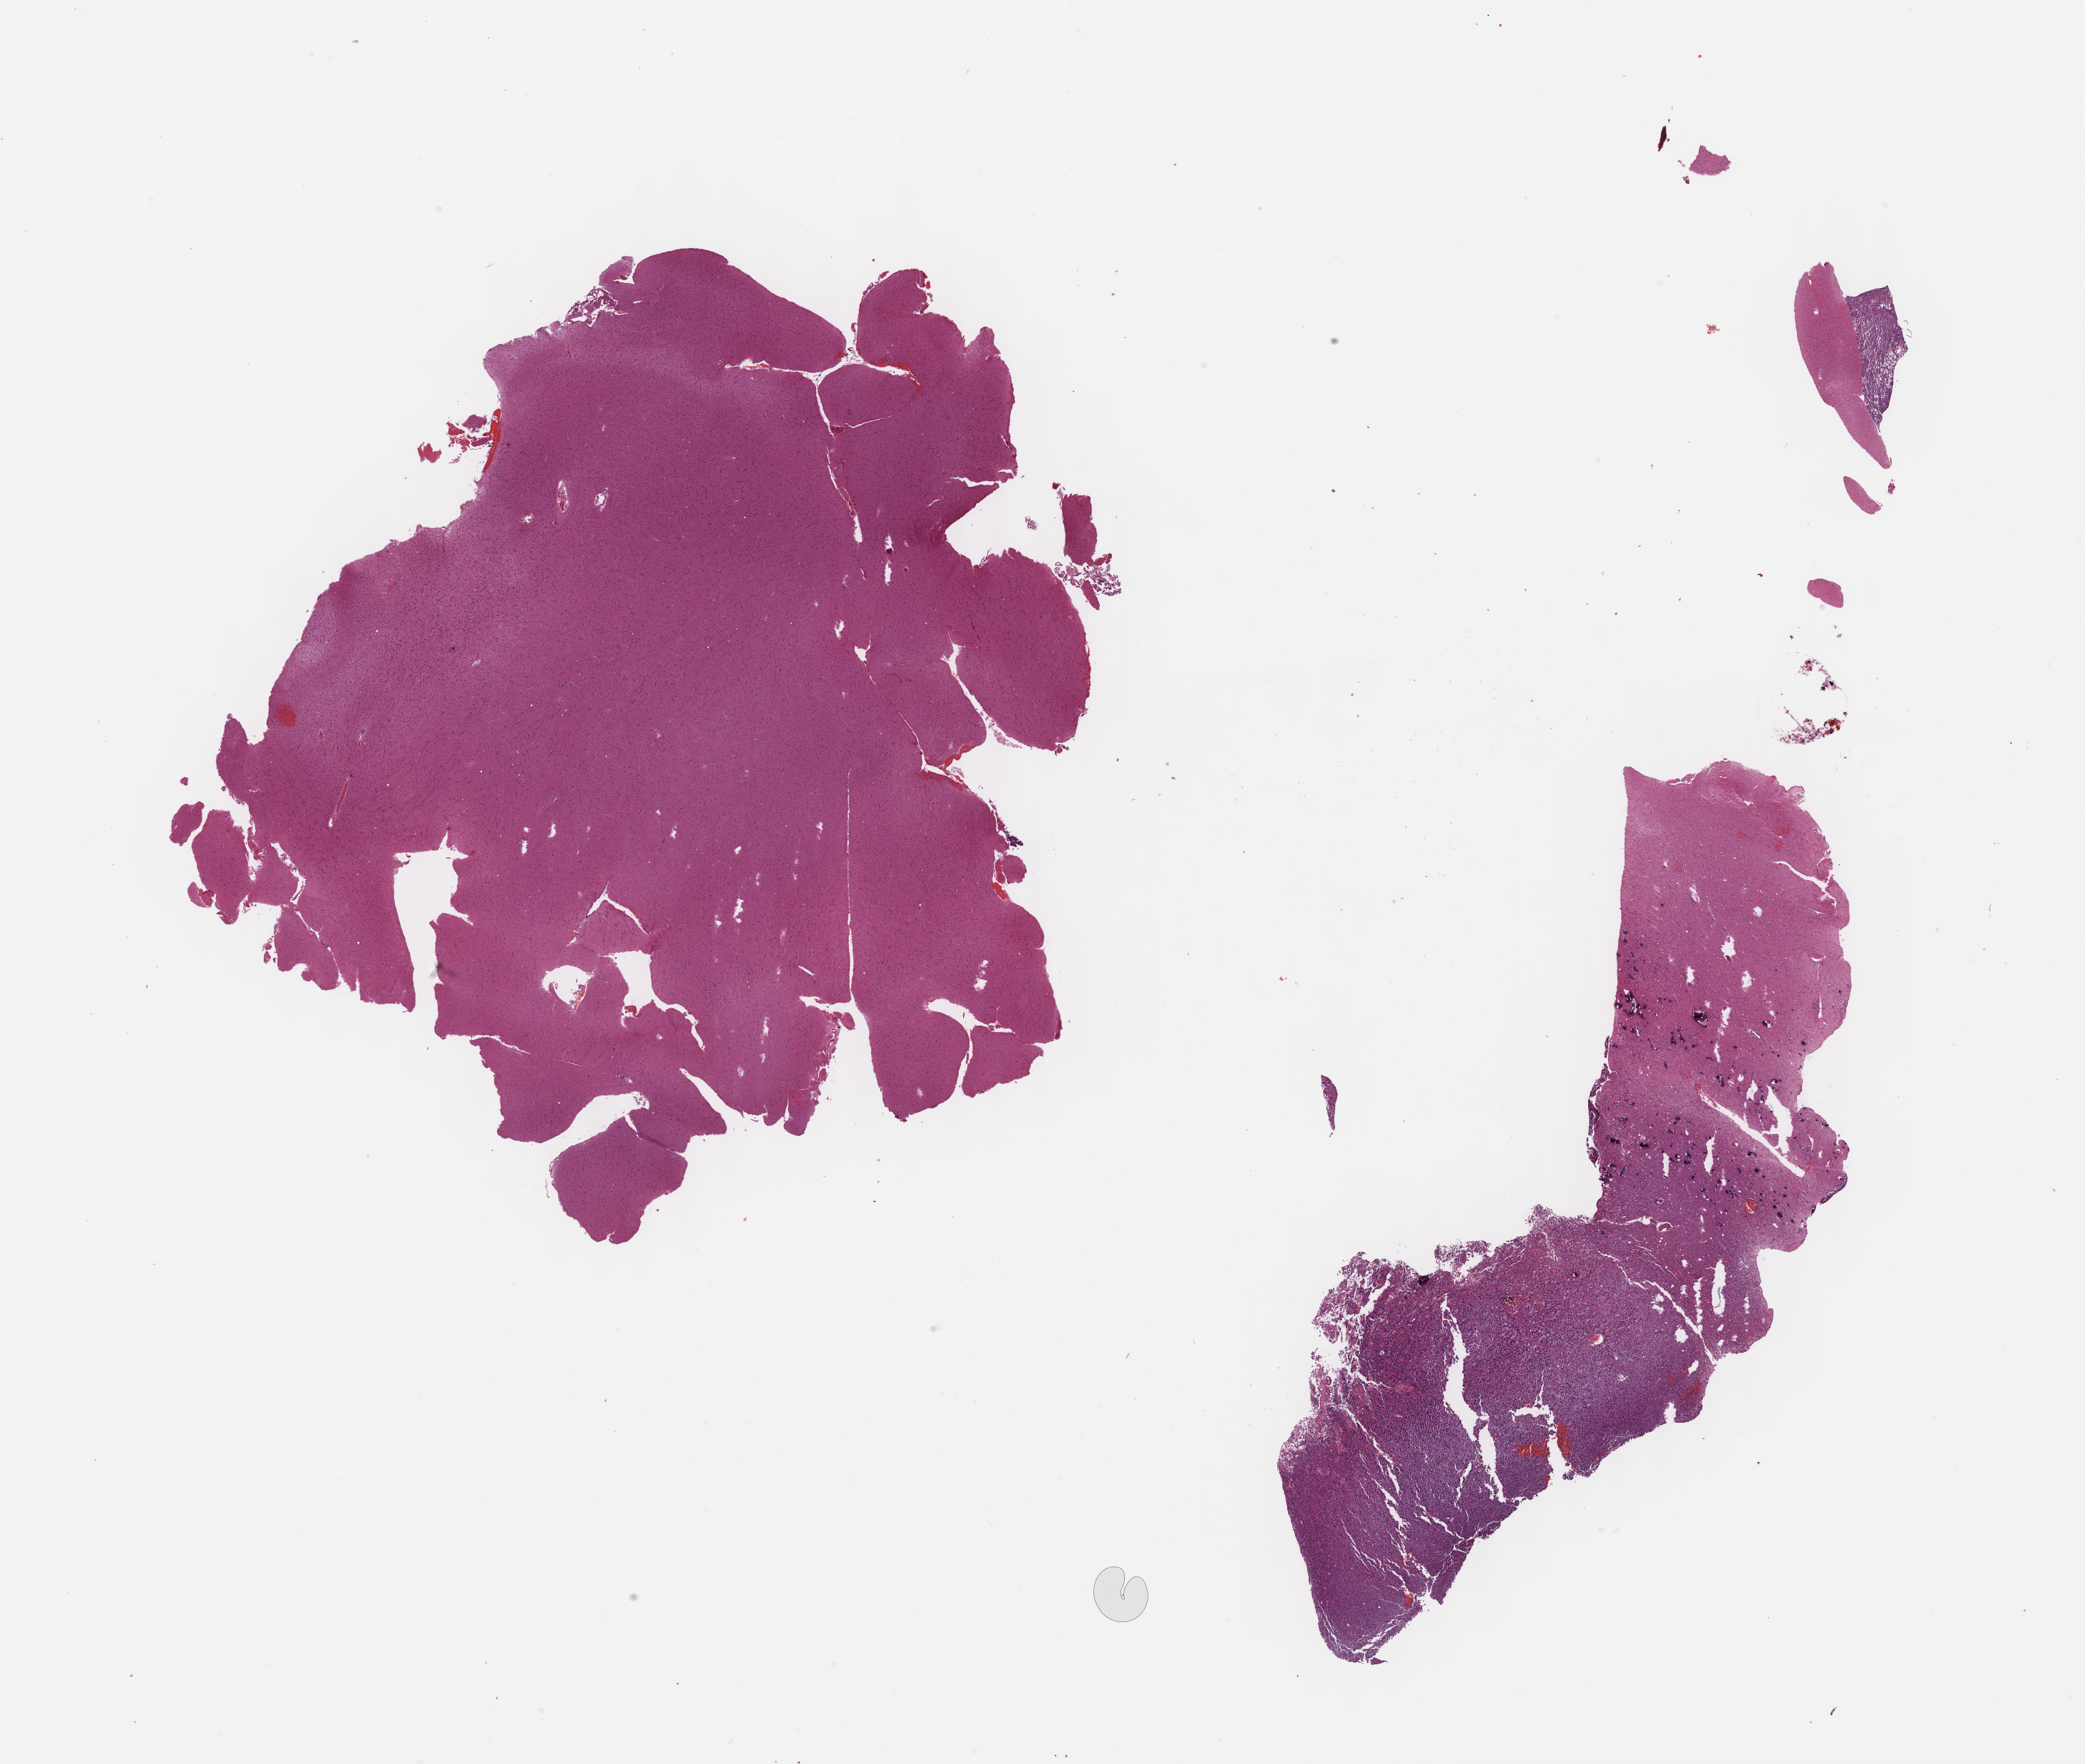
Whole-slide histology image, Hematoxylin and eosin (H&E) stained, a low-resolution overview of the entire scanned area, about 23.7 x 20.0 mm (slide scanned at 40x). Formalin-fixed paraffin-embedded (FFPE) diagnostic section. Brain, primary tumour sample. Male, age 40 years at initial diagnosis. Histologic grade: G3 (poorly differentiated).
Laterality: left. Pathologic diagnosis: Oligodendroglioma, anaplastic.